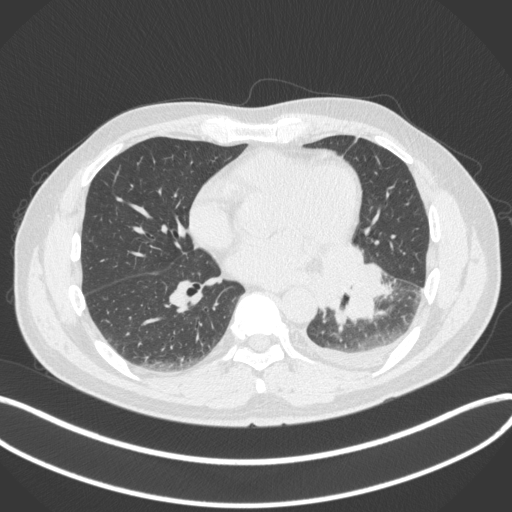
Chest CT, one axial slice. Position 158 of 350 along the scan axis. Lung window (W 1500 / L -600 HU). 1 mm slice thickness. 512 × 512 image matrix, field of view 400 × 400 mm. Male patient, age 58 years. From the clinical record (not read from this slice): clinical TNM (as recorded): T3 N1 M1b.
Structures marked on this image (bounding box drawn by a radiologist):
- lung tumour (recorded histology: small cell carcinoma): bounding box [x1, y1, x2, y2] px = [315, 239, 388, 332]